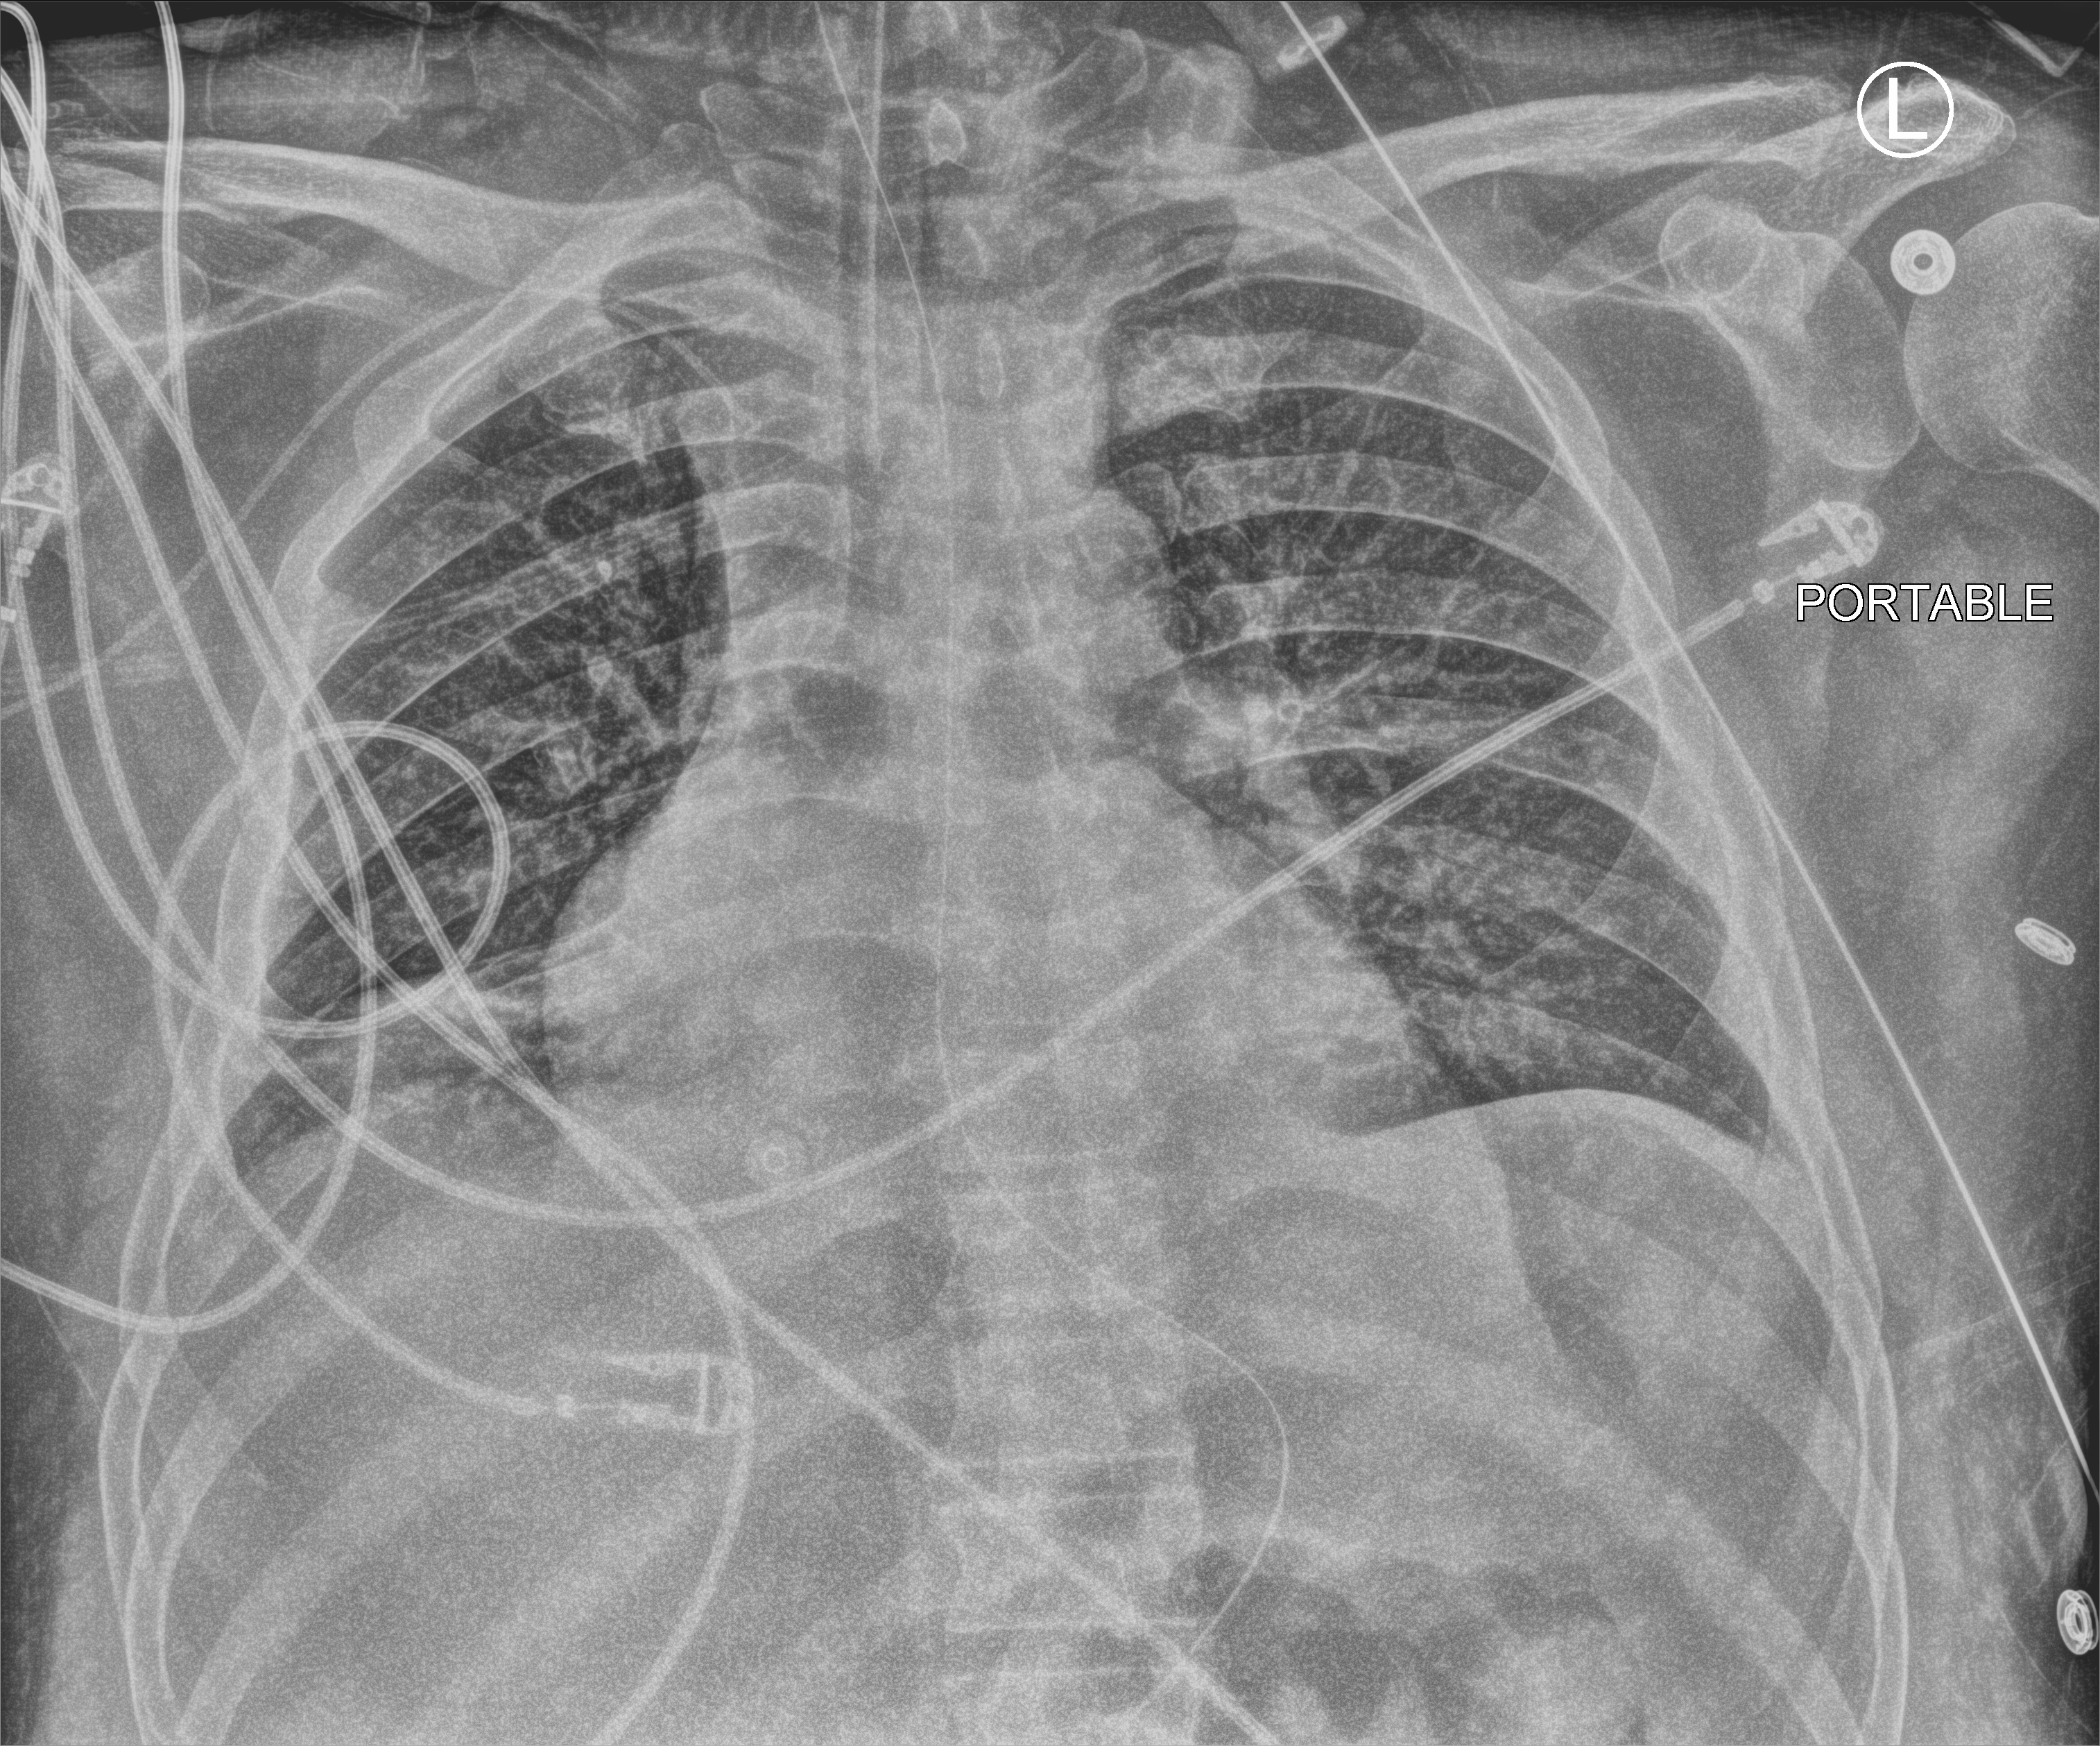
Portable chest radiograph, anteroposterior (AP) projection. Male patient hospitalised with COVID-19, age 18–59 years.
From the hospital-stay record, not from the radiograph (when in the stay this image was taken is not recorded): admitted to intensive care during this hospital stay: yes; mechanically ventilated during this hospital stay: yes.